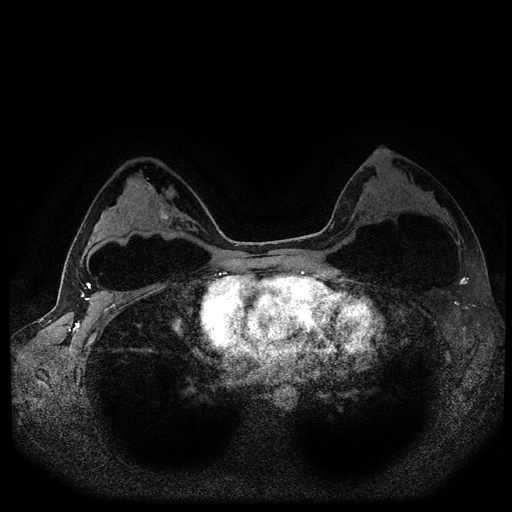
Breast MRI (dynamic contrast-enhanced, multi-phase), one axial slice. Slice 65 of 116 in the series (ordered by position). Dynamic contrast-enhanced series, time point 2 of 5 at this slice position (early post-contrast). 1.5 T. TE 2.6 ms, TR 5.4 ms. 2 mm slice thickness. 512 × 512 image matrix, field of view 340 × 340 mm. Female patient, age 33 years.
Outlined on this slice (semi-automatically segmented with operator editing):
- breast lesion (labelled benign in the annotation): box from (x=158, y=206) to (x=172, y=222) px